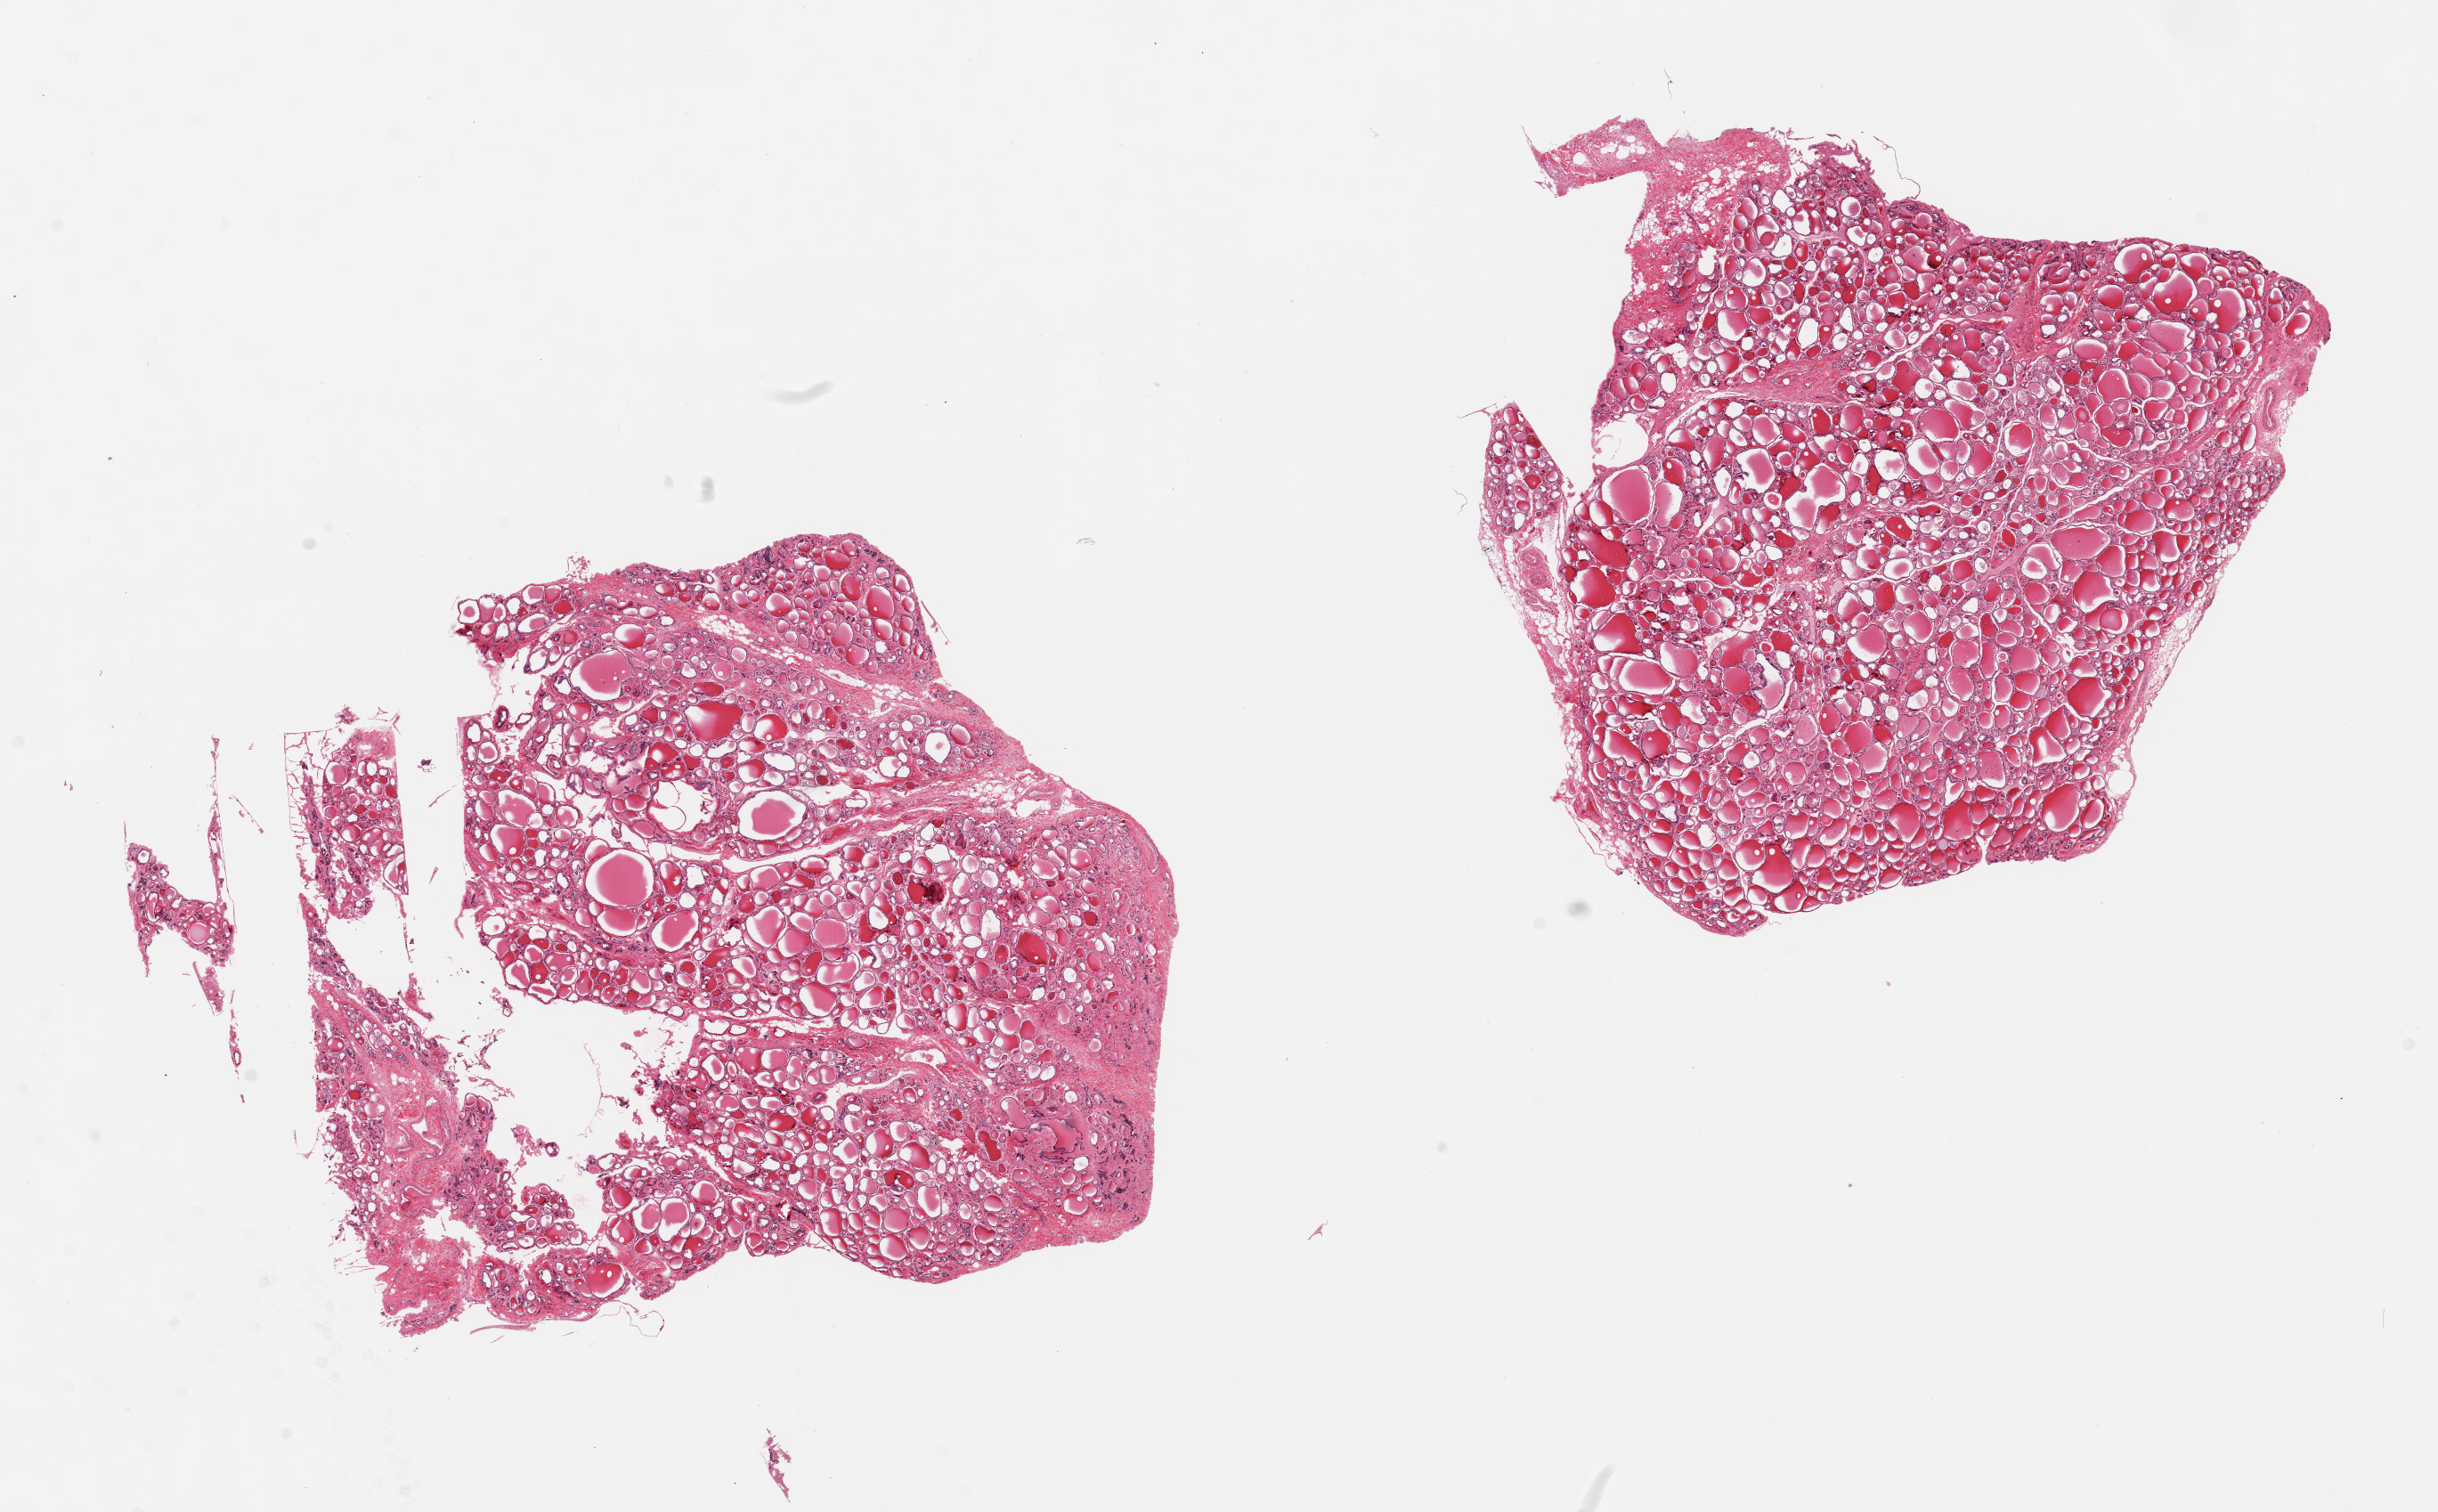
H&E whole-slide image, low-resolution overview of the scanned area, about 21.7 x 13.4 mm, PAXgene-fixed, paraffin-embedded tissue, target tissue: thyroid, donor tissue sample. Donor sex: male.
Reviewer comment on this tissue sample: 2 pieces; some fibrosis.